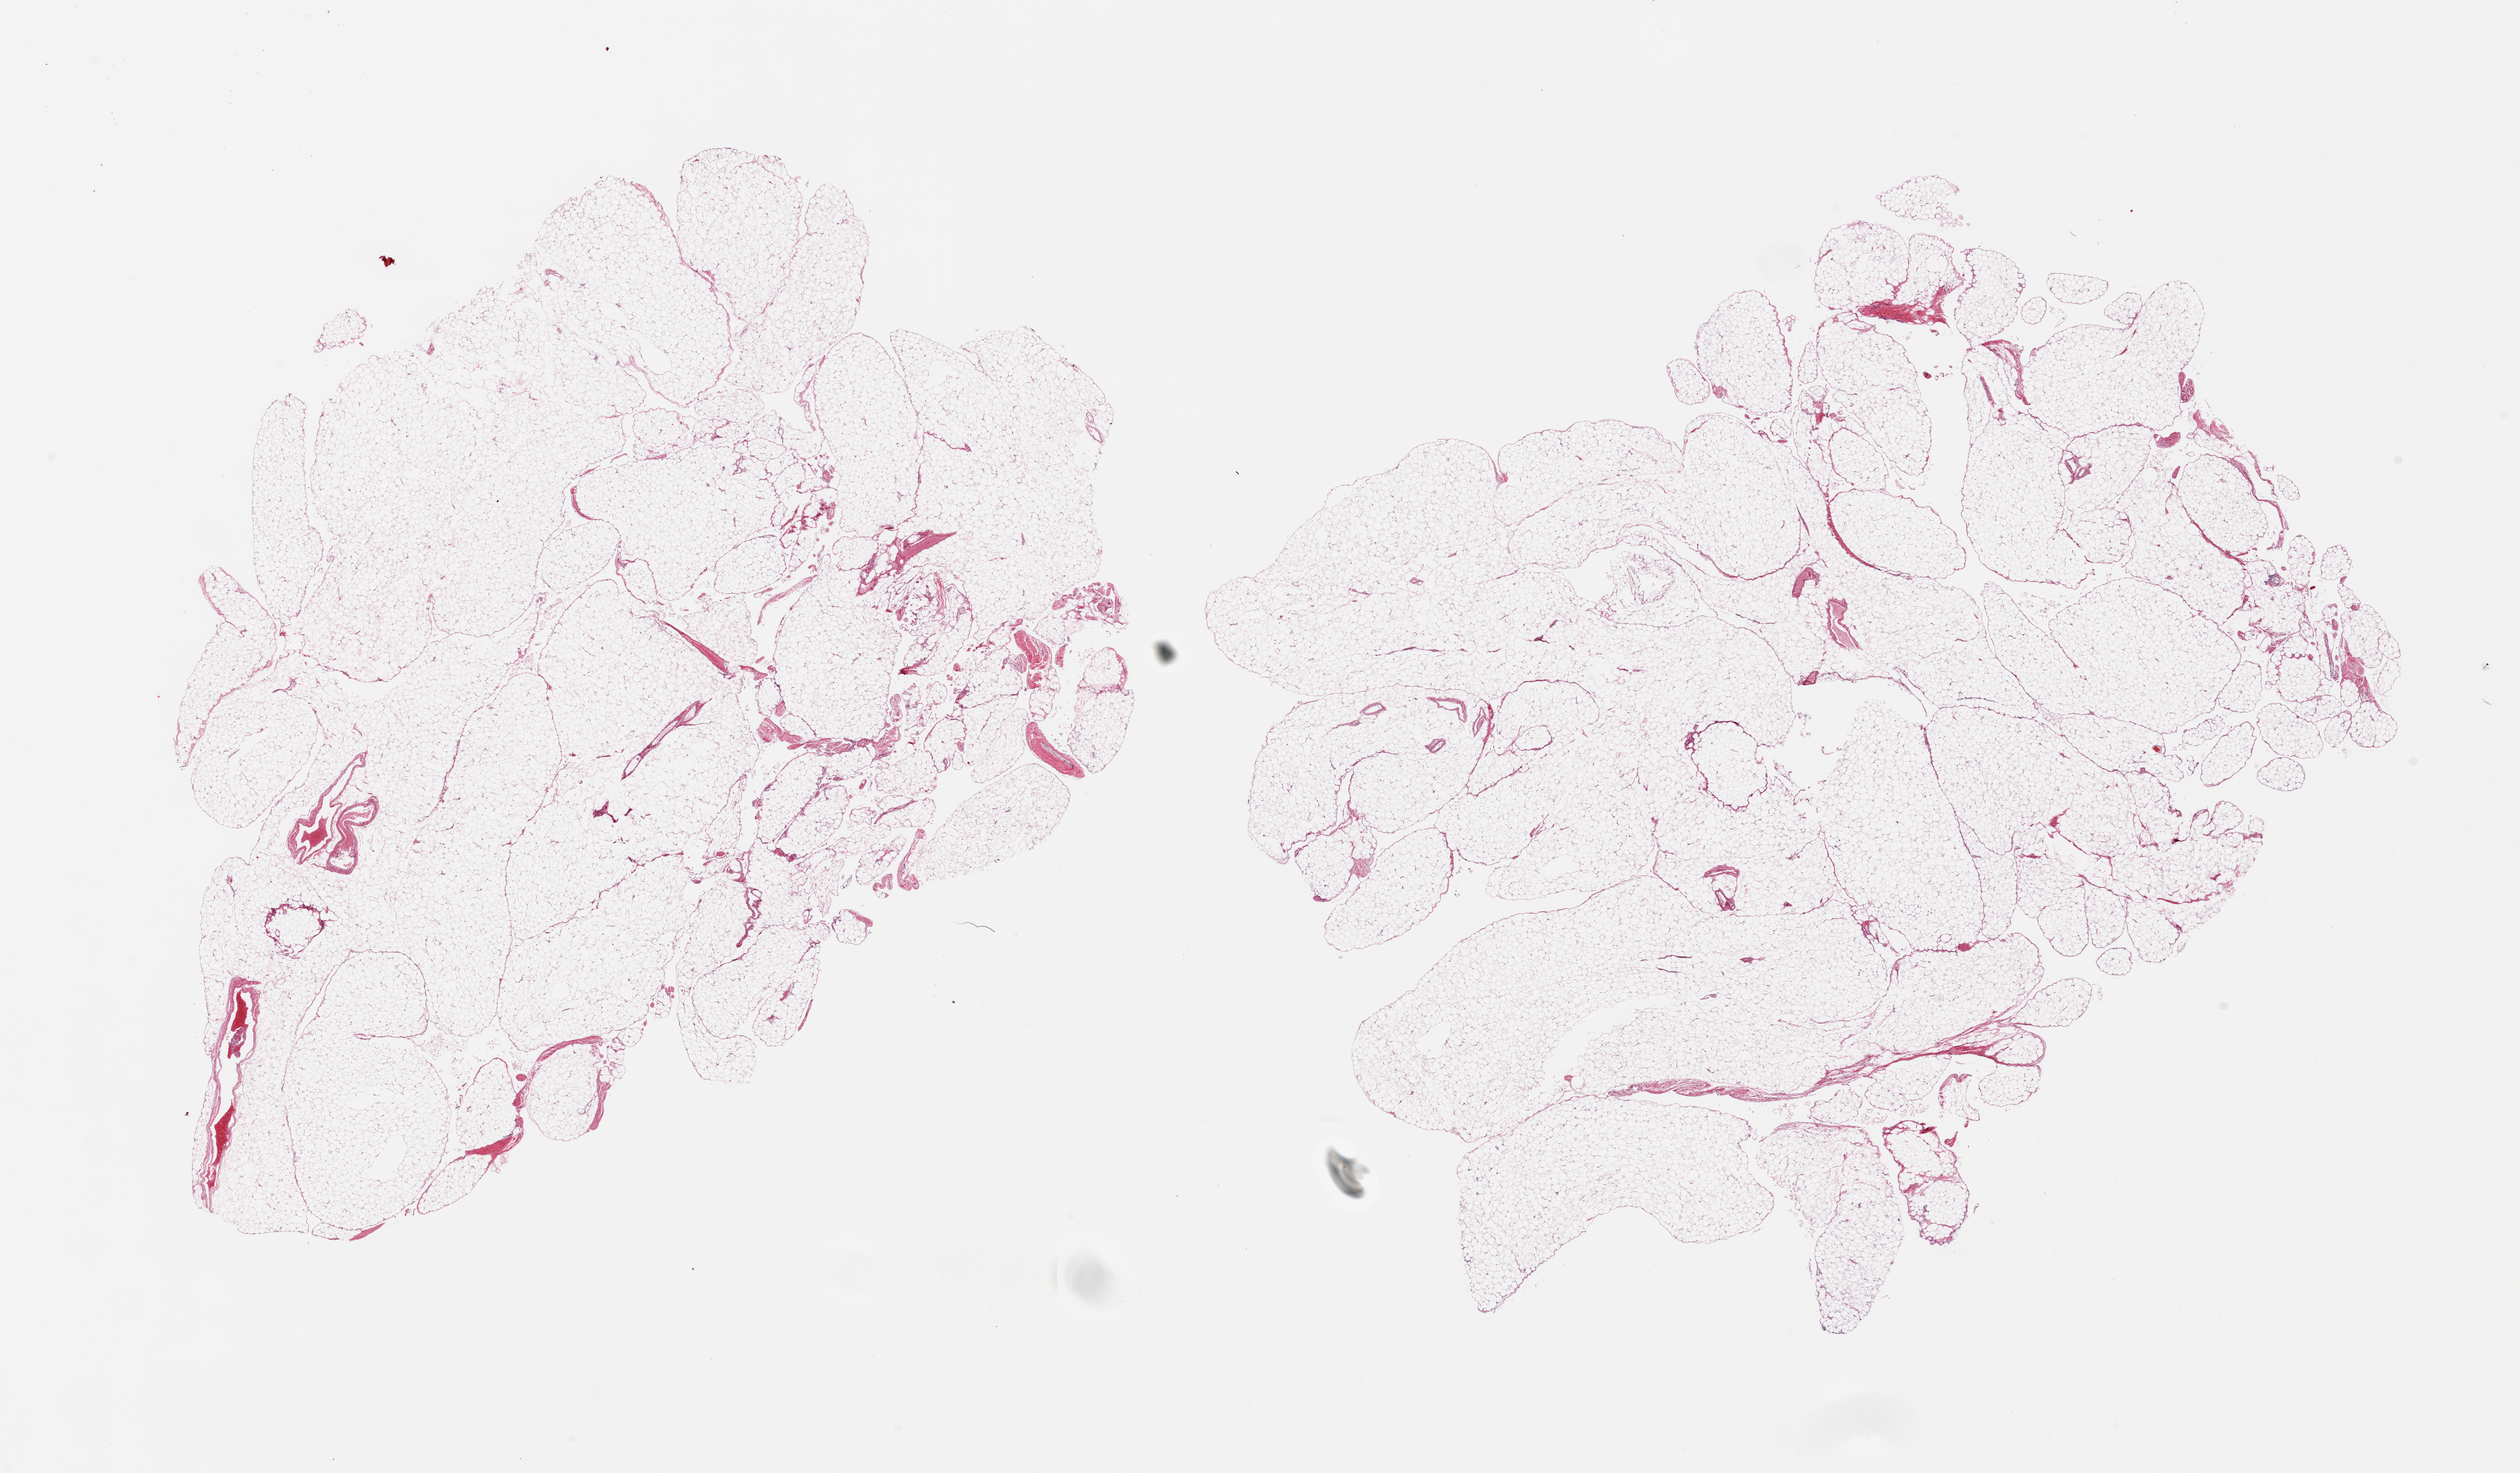
Digitized haematoxylin and eosin-stained section, low-resolution overview of the scanned area, about 30.5 x 17.8 mm (slide scanned at 20x). PAXgene-fixed, paraffin-embedded tissue. Section of omentum (target tissue). Donor tissue sample. Donor sex: female.
Review note (as recorded): 2 pieces, ~5-10% vascular elements.